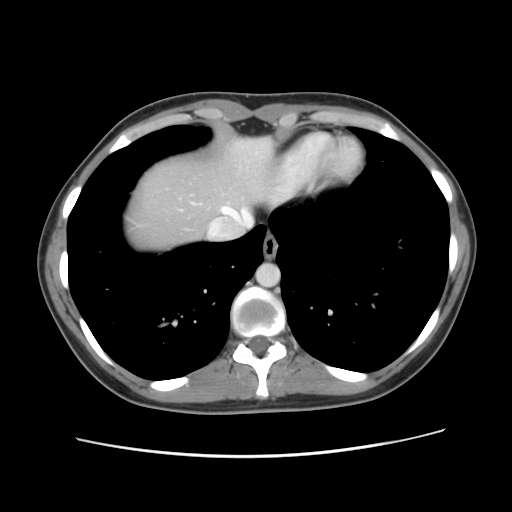
Contrast-enhanced abdominal CT, one axial slice; 120 kVp; intravenous contrast given; soft-tissue window (W 400 / L 40 HU); 2.5 mm slice thickness; 512 × 512 image matrix, field of view 339 × 339 mm. Female patient, age 33 years. Case-level facts recorded for this patient, not image findings: diagnosis: colorectal cancer liver metastases, imaged before liver resection; multiple liver metastases: yes; largest metastasis: 4.5 cm; disease in both lobes: yes.
Annotated regions visible in this slice (outlined manually by an expert reader):
- hepatic veins: bounding box <222,206,253,226> (left, top, right, bottom; pixels)
- liver: <124,137,285,251>
- planned liver remnant (the part of the liver to remain after resection): <124,138,285,251>